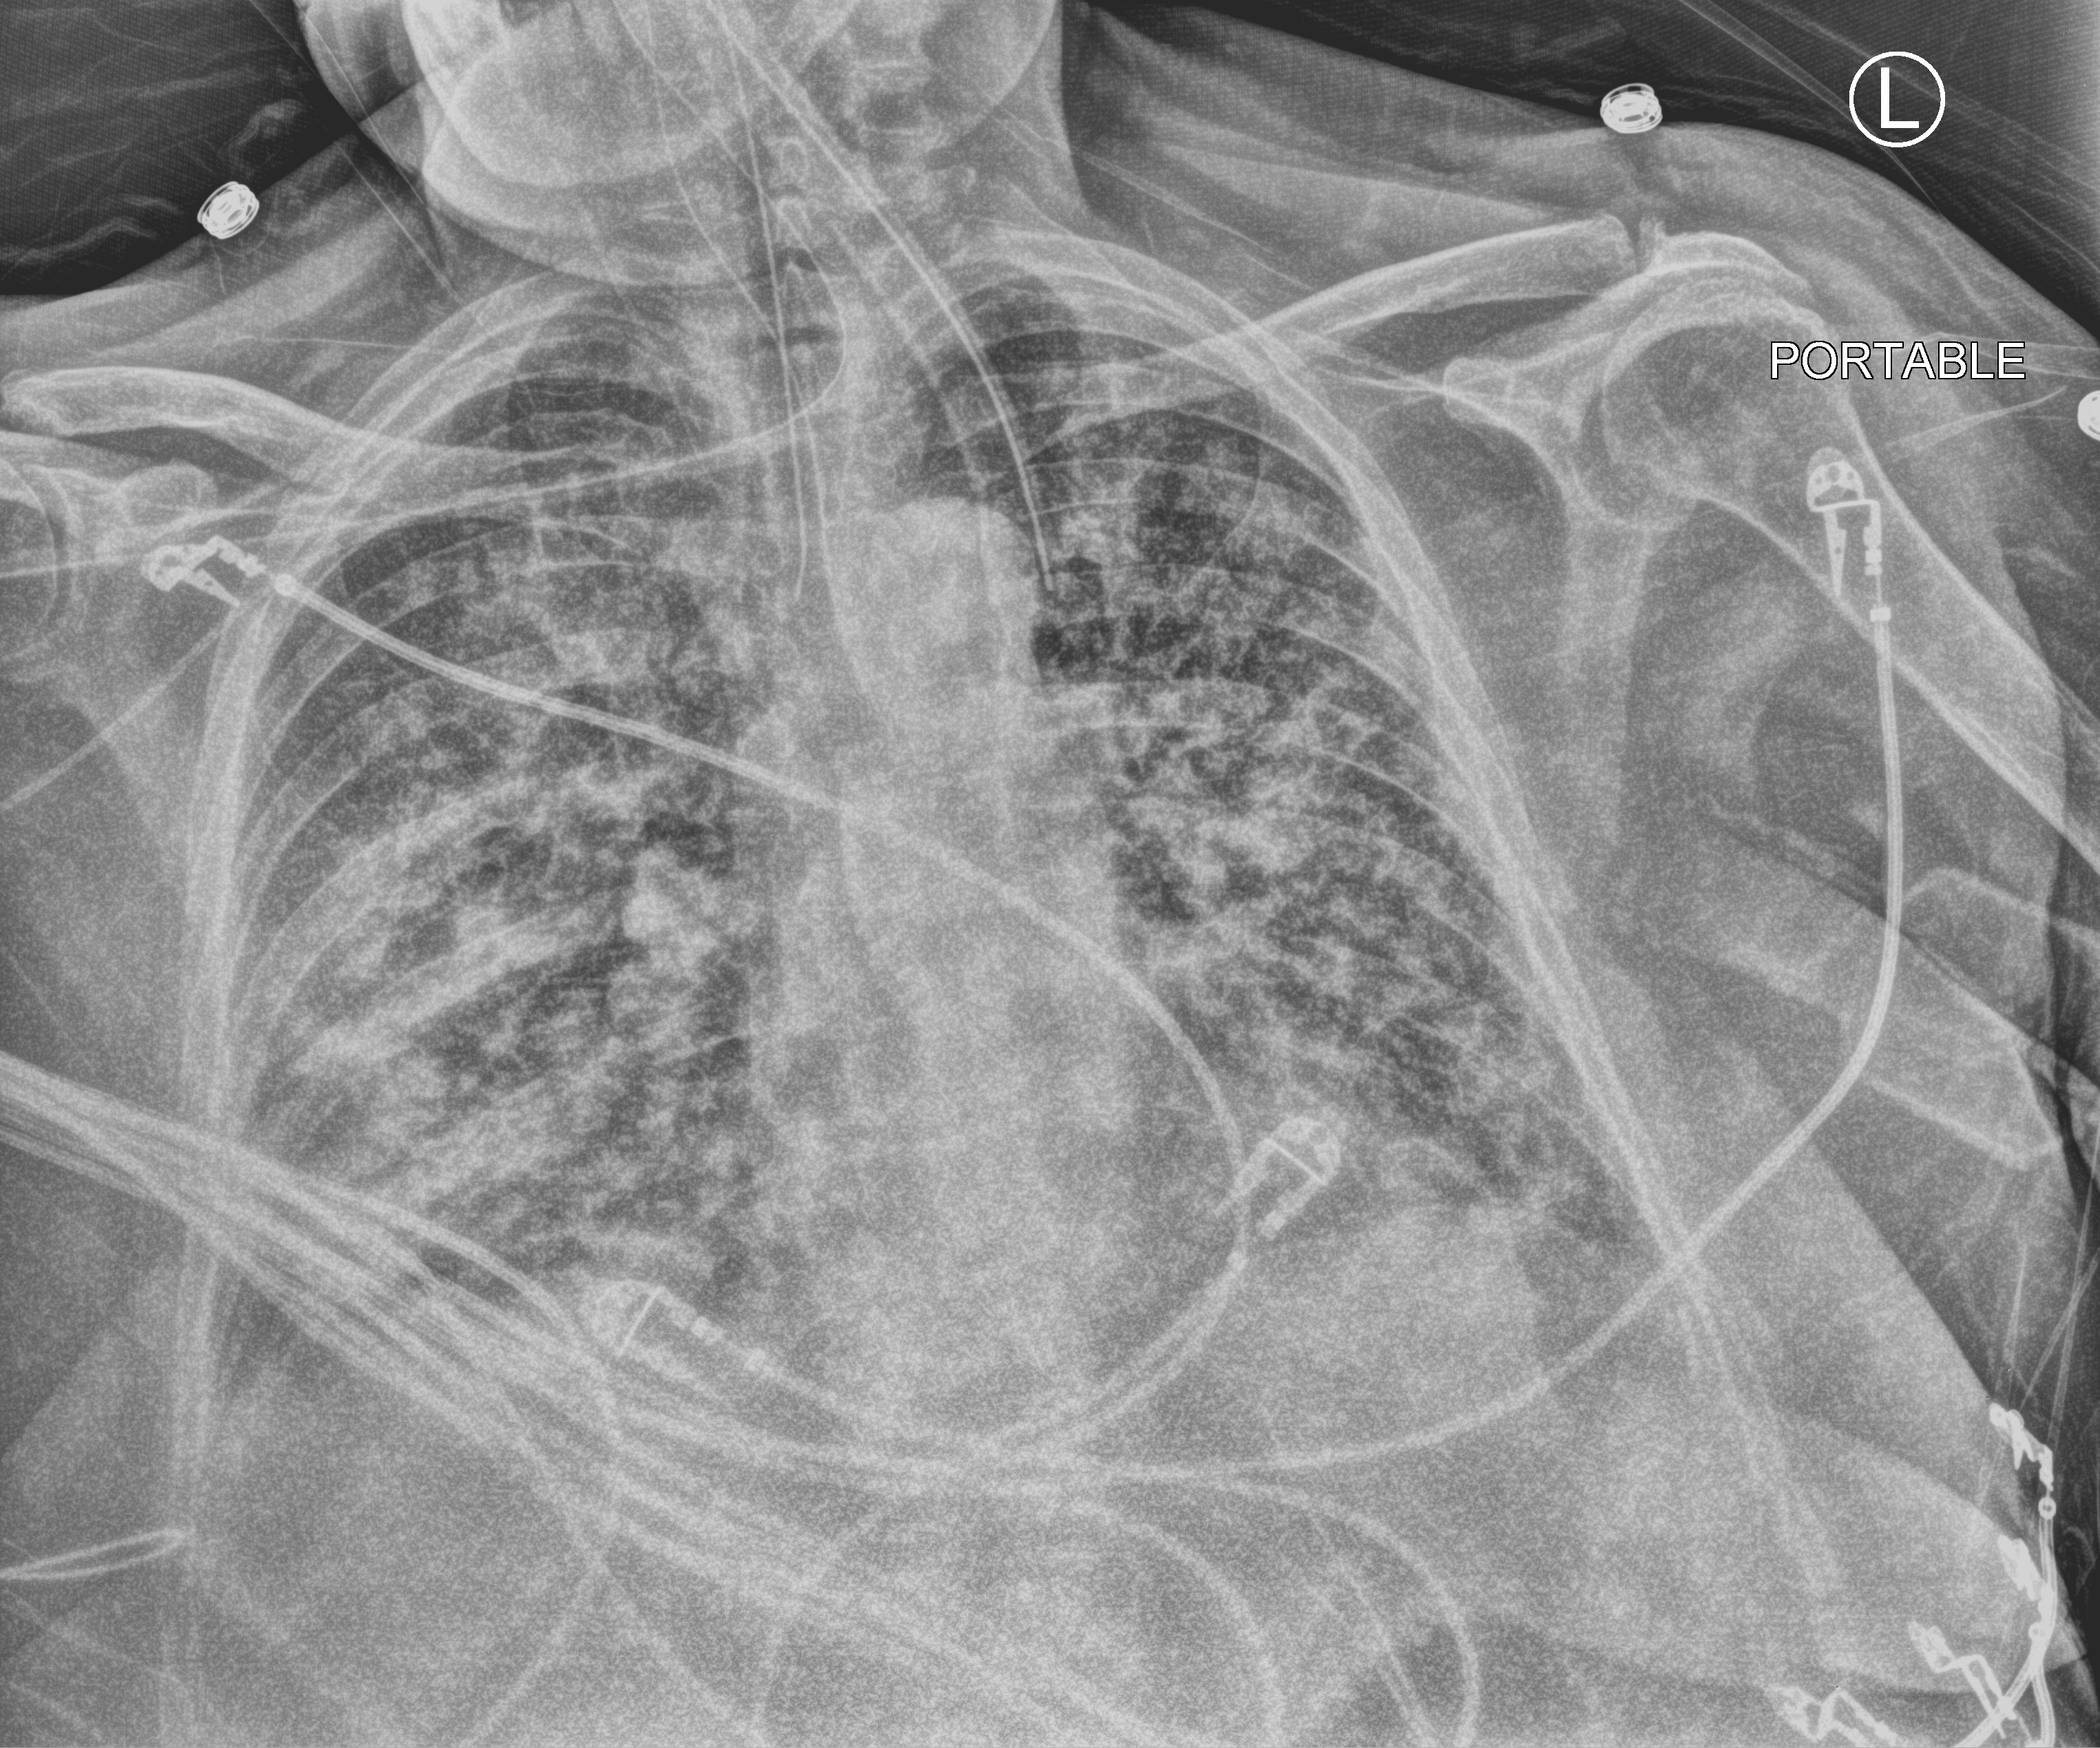
Chest X-ray (portable); anteroposterior (AP) projection. Female patient hospitalised with COVID-19, age 60–74 years.
Hospital-stay facts (about this admission, not read from this image; timing relative to this image not recorded):
- mechanically ventilated during this hospital stay: yes
- hypertension (admission record): yes